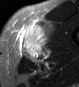
MRI of an extremity soft-tissue mass, one axial slice; slice 30 of 45 in the series (ordered by position); STIR; MR volume resampled by the dataset authors to the PET/CT grid (not the native acquisition matrix); 3.27 mm slice thickness; 79 × 87 image matrix, field of view 77 × 85 mm. Male patient. Case-level facts recorded for this patient, not image findings: histological type: pleiomorphic leiomyosarcoma; grade: high; site of the primary tumour: left thigh.
Annotated regions visible in this slice (expert contour drawn on MRI and transferred to this co-registered scan by the dataset authors):
- gross tumour volume including surrounding oedema: bounding box [x1, y1, x2, y2] px = [20, 21, 53, 60]
- gross tumour volume (mass): [22, 27, 46, 58]